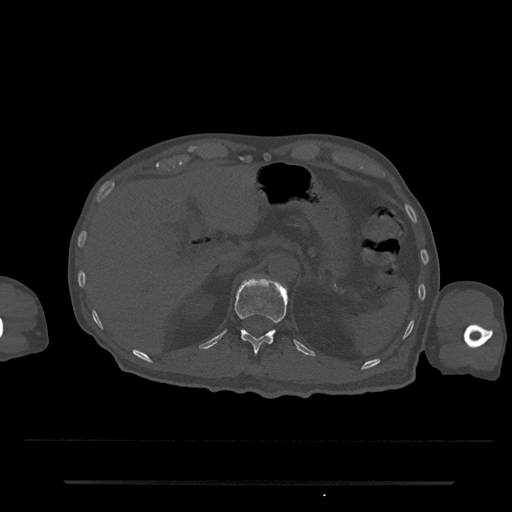
CT including the spine, one axial slice; slice 189 of 797 in the series (ordered by position); reconstruction kernel Br40s/3; 120 kVp; bone window (W 1800 / L 400 HU); 0.5 mm slice thickness; 512 × 512 image matrix, field of view 427 × 427 mm. Patient: male, 74 years. From the clinical record (not read from this slice): primary cancer: prostate.
Annotated regions visible in this slice (semi-automatically segmented with operator editing):
- T12 vertebra: bounding box (x1, y1, x2, y2) in pixels: (235, 278, 288, 354)